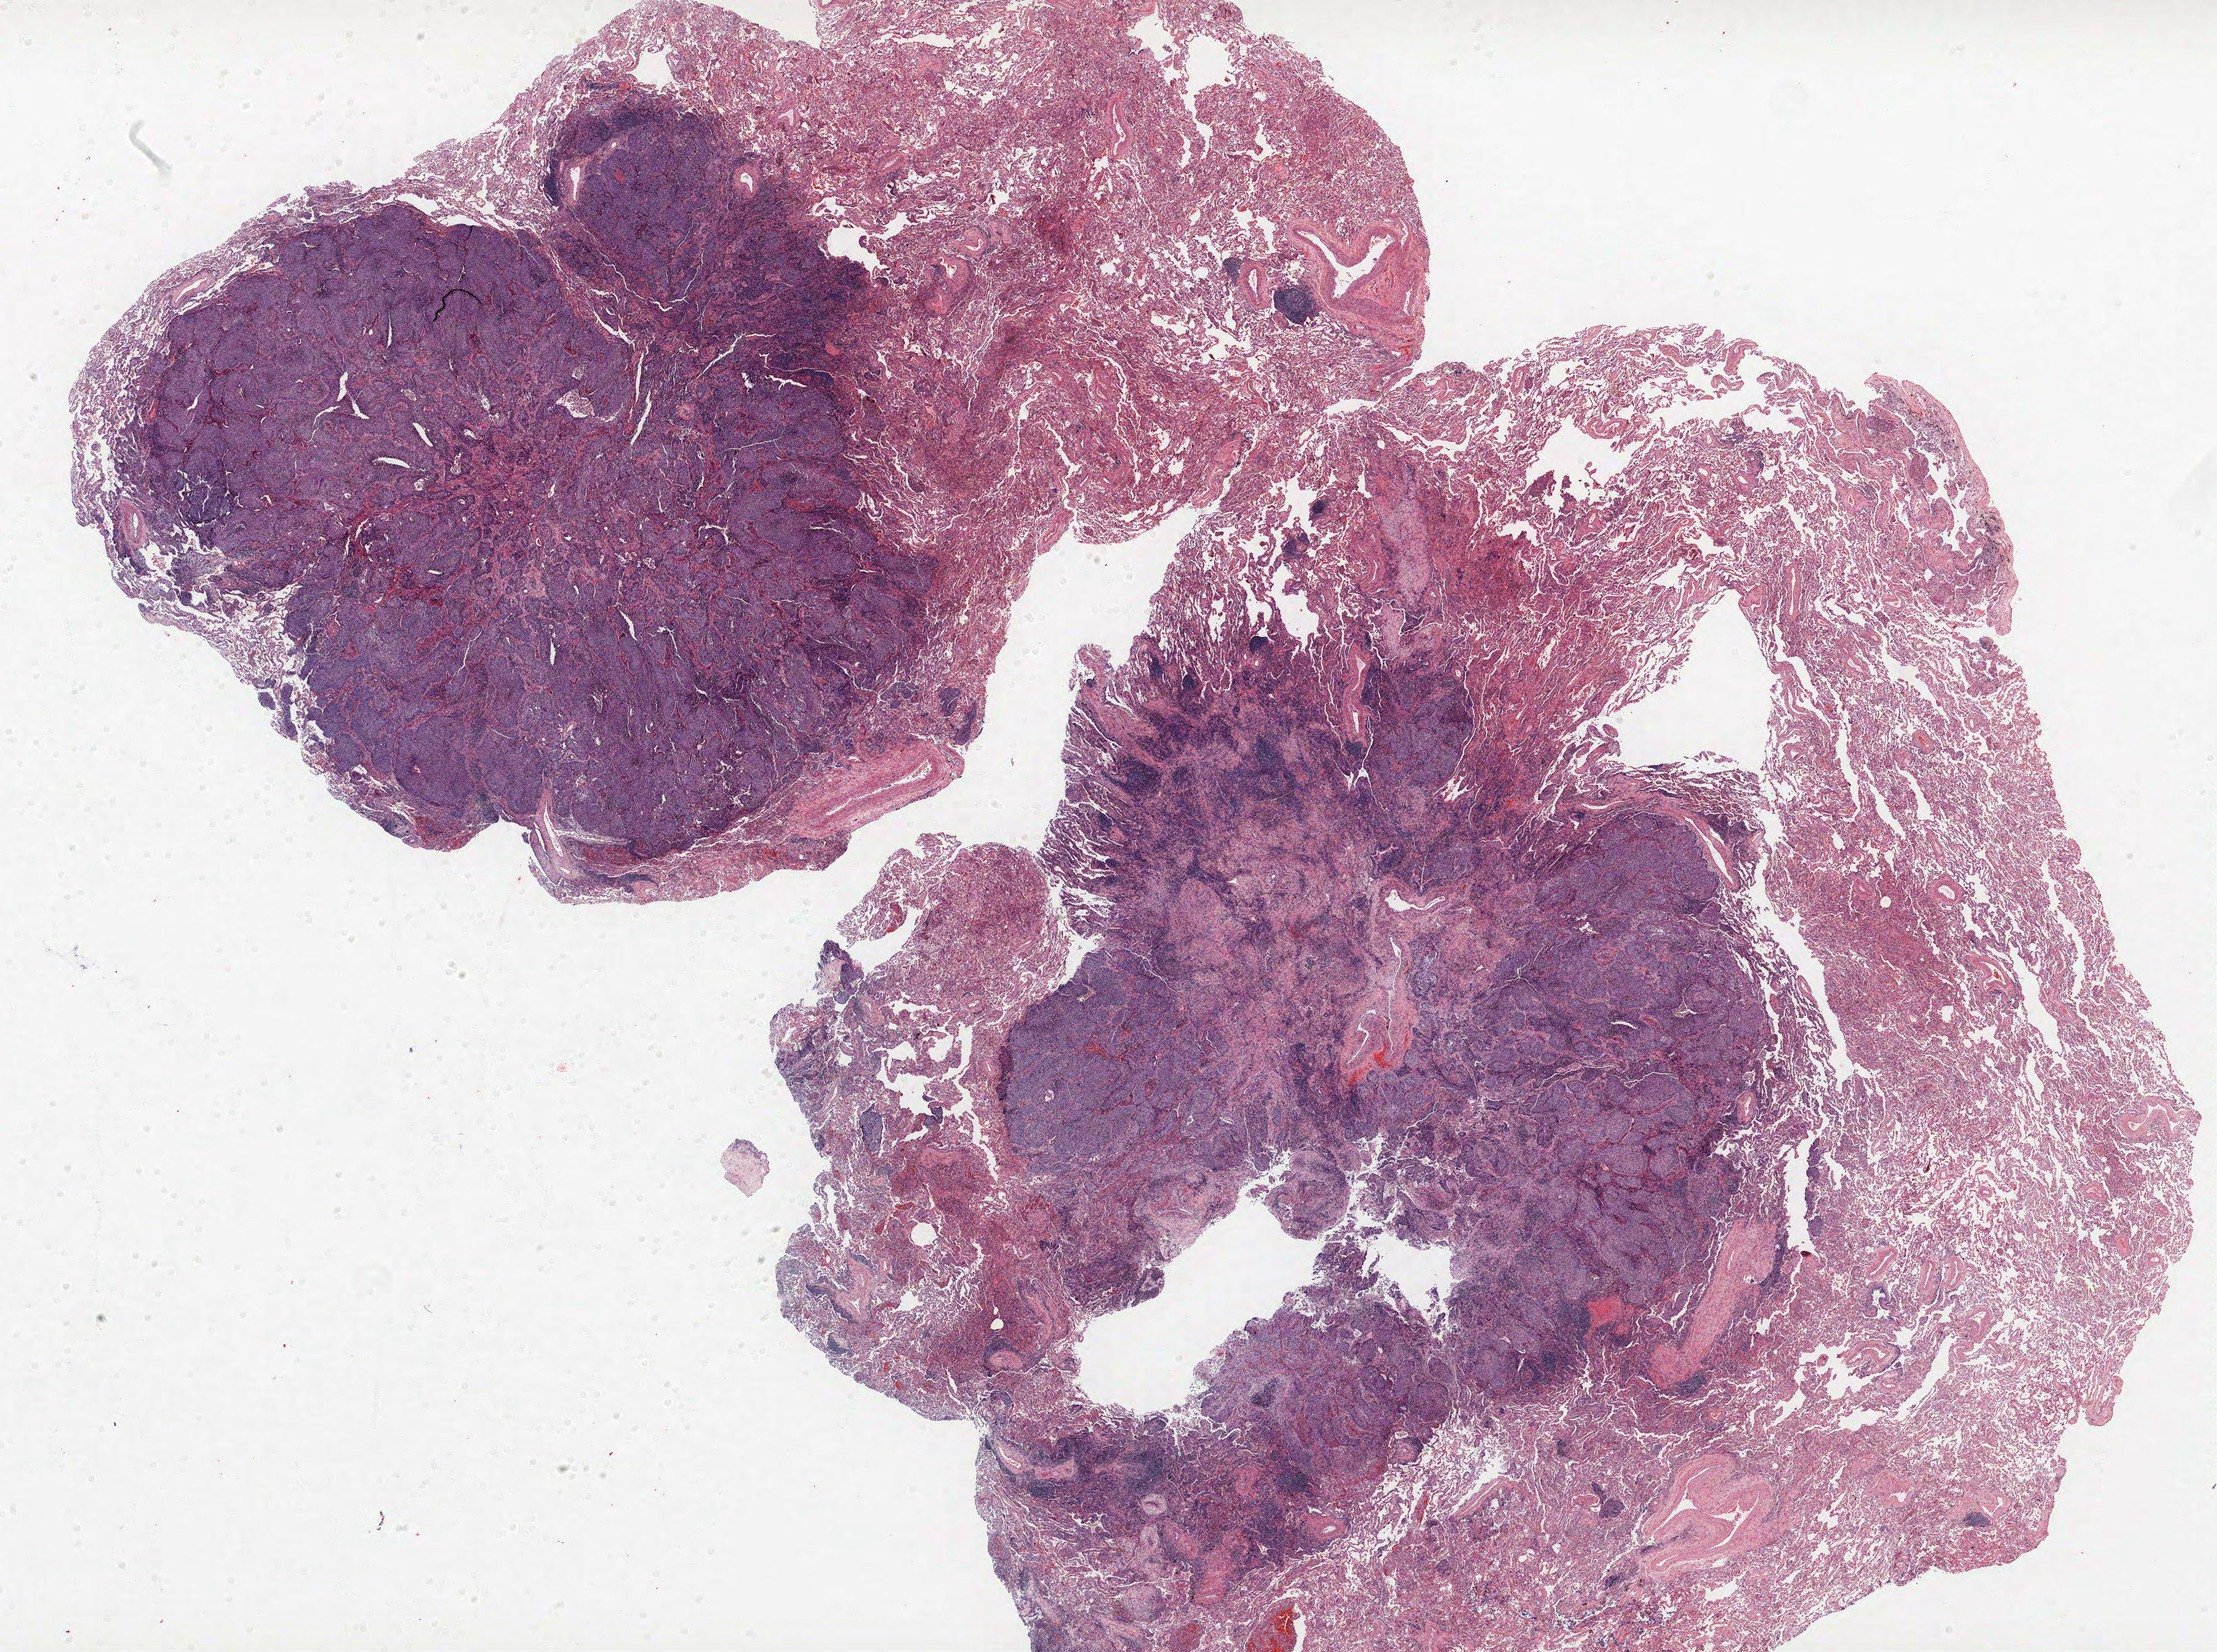
H&E-stained whole-slide image, a low-resolution overview of the entire scanned area, about 28.1 x 20.9 mm (from a 40x scan); FFPE section; lung tissue. Male, age 59 at enrolment. Former smoker at enrolment. Grade: moderately differentiated (G2).
- tumour size (pathology): 15 mm
- stage (AJCC 6th edition): IA
- participant's lung-cancer diagnosis: Squamous cell carcinoma, NOS
- primary tumour location (clinical record): right lower lobe